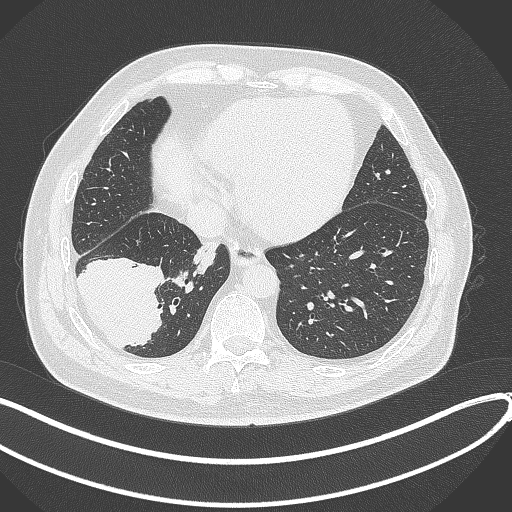
Chest CT, one axial slice; slice 101 of 360 in the series (ordered by position); reconstruction kernel B70f; lung window (W 1500 / L -600 HU); 1 mm slice thickness; 512 × 512 image matrix, field of view 400 × 400 mm. Patient: male, 59 years.
Annotated regions visible in this slice (rectangle marked by the reading radiologist):
- lung tumour (recorded histology: adenocarcinoma): box from (x=76, y=256) to (x=166, y=350) px